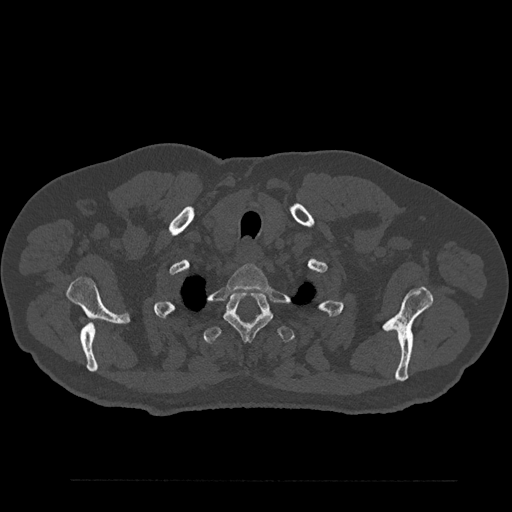
CT including the spine, one axial slice; 120 kVp; bone window (W 1800 / L 400 HU); 0.5 mm slice thickness; 512 × 512 image matrix, field of view 430 × 430 mm. Patient: male, 61 years. Case-level facts recorded for this patient, not image findings: primary cancer: prostate.
Structures marked on this image (semi-automatic segmentation, software-assisted and operator-edited):
- T1 vertebra: bounding box [x1, y1, x2, y2] px = [227, 264, 270, 292]
- T2 vertebra: [223, 292, 273, 341]
- T3 vertebra: [203, 326, 294, 345]